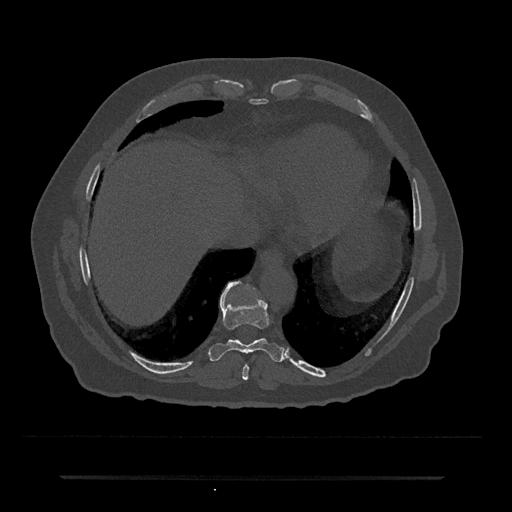
CT including the spine, one axial slice. Position 277 of 797 along the scan axis. Reconstruction kernel Br40s/3. 120 kVp. Bone window (W 1800 / L 400 HU). 0.5 mm slice thickness. 512 × 512 image matrix. Patient: male, 69 years. Case-level facts recorded for this patient, not image findings: primary cancer: prostate.
Annotated regions visible in this slice (semi-automatically segmented with operator editing):
- T10 vertebra: bounding box (x1, y1, x2, y2) in pixels: (246, 285, 248, 287)
- T8 vertebra: (242, 365, 249, 380)
- T9 vertebra: (209, 282, 285, 362)